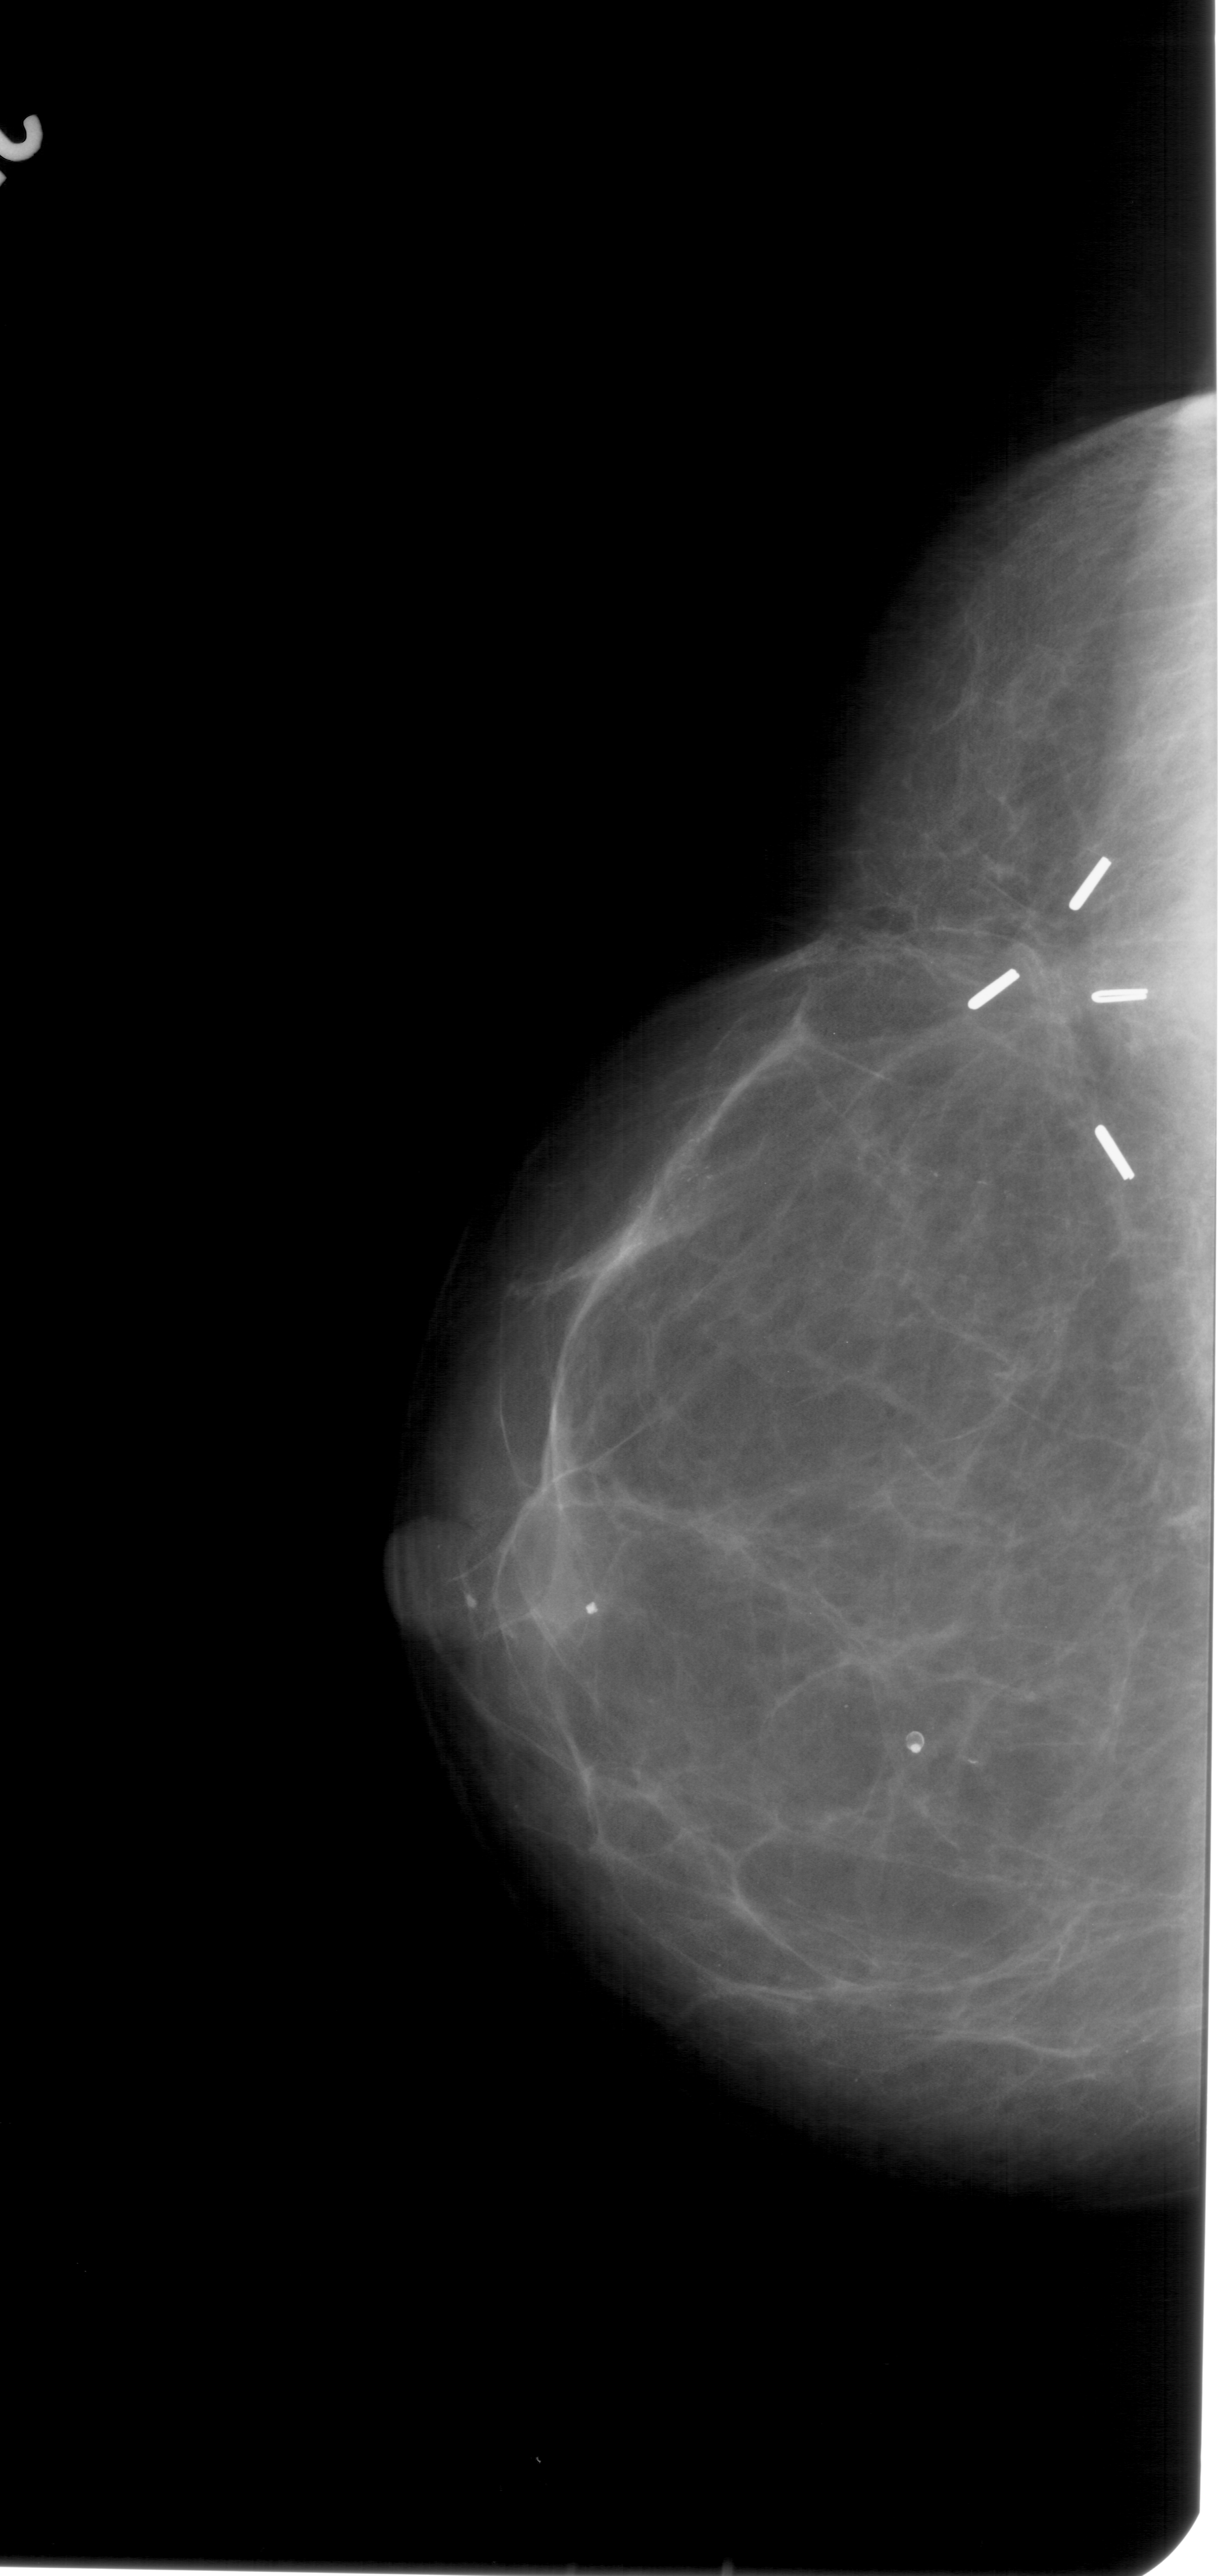
Scanned film-screen mammogram; left breast; CC view.
Abnormality record for this image: calcifications, morphology pleomorphic, distribution linear; BI-RADS assessment category 5; subtlety rating 4 on a 1 (subtle) to 5 (obvious) scale; pathology (as recorded): malignant.